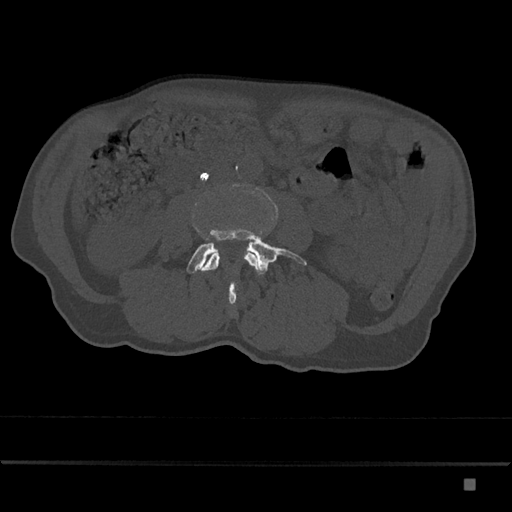
CT including the spine, one axial slice. Position 366 of 797 along the scan axis. 120 kVp. Bone window (W 1800 / L 400 HU). 0.5 mm slice thickness. 512 × 512 image matrix, field of view 390 × 390 mm. Male patient, age 72 years. Case-level facts recorded for this patient, not image findings: primary cancer: prostate.
Structures marked on this image (semi-automatically segmented with operator editing):
- L3 vertebra: bounding box <202,253,258,271> (left, top, right, bottom; pixels)
- L4 vertebra: <187,228,307,304>